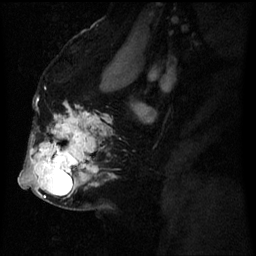
Breast MRI (dynamic contrast-enhanced), one sagittal slice. Slice 37 of 60 in the series (ordered by position). Dynamic contrast-enhanced series, image 2 of 3 at this slice position (ordered by acquisition). 1.5 T. TE 4.2 ms, TR 8 ms. 2.5 mm slice thickness. 256 × 256 image matrix. Patient: female, 50 years.
Annotated regions visible in this slice (semi-automatic segmentation, software-assisted and operator-edited):
- analysis volume of interest (the breast-tissue region the enhancement analysis was run in; not a lesion): bounding box (x1, y1, x2, y2) in pixels: (24, 118, 97, 203)
- tumour enhancement mask (voxels above the 70 % enhancement threshold inside the analysis volume of interest): (31, 124, 93, 171)